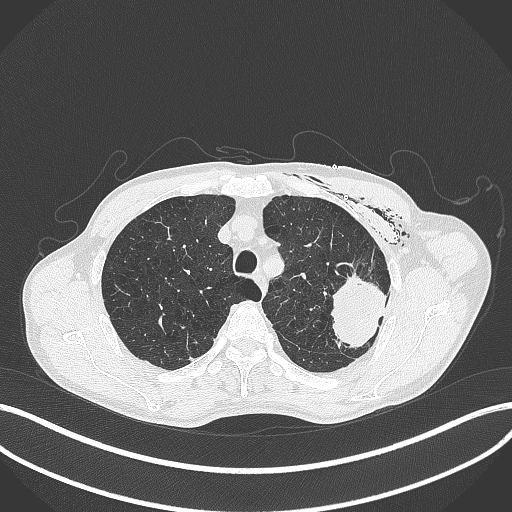
Chest CT, one axial slice. Slice 322 of 457 in the series (ordered by position). Lung window (W 1500 / L -600 HU). 1 mm slice thickness. 512 × 512 image matrix, field of view 400 × 400 mm. Male patient, age 58 years. From the clinical record (not read from this slice): clinical TNM (as recorded): T3 N0 M0.
Annotated regions visible in this slice (rectangle marked by the reading radiologist):
- lung tumour (recorded histology: adenocarcinoma): bounding box (x1, y1, x2, y2) in pixels: (324, 261, 391, 352)